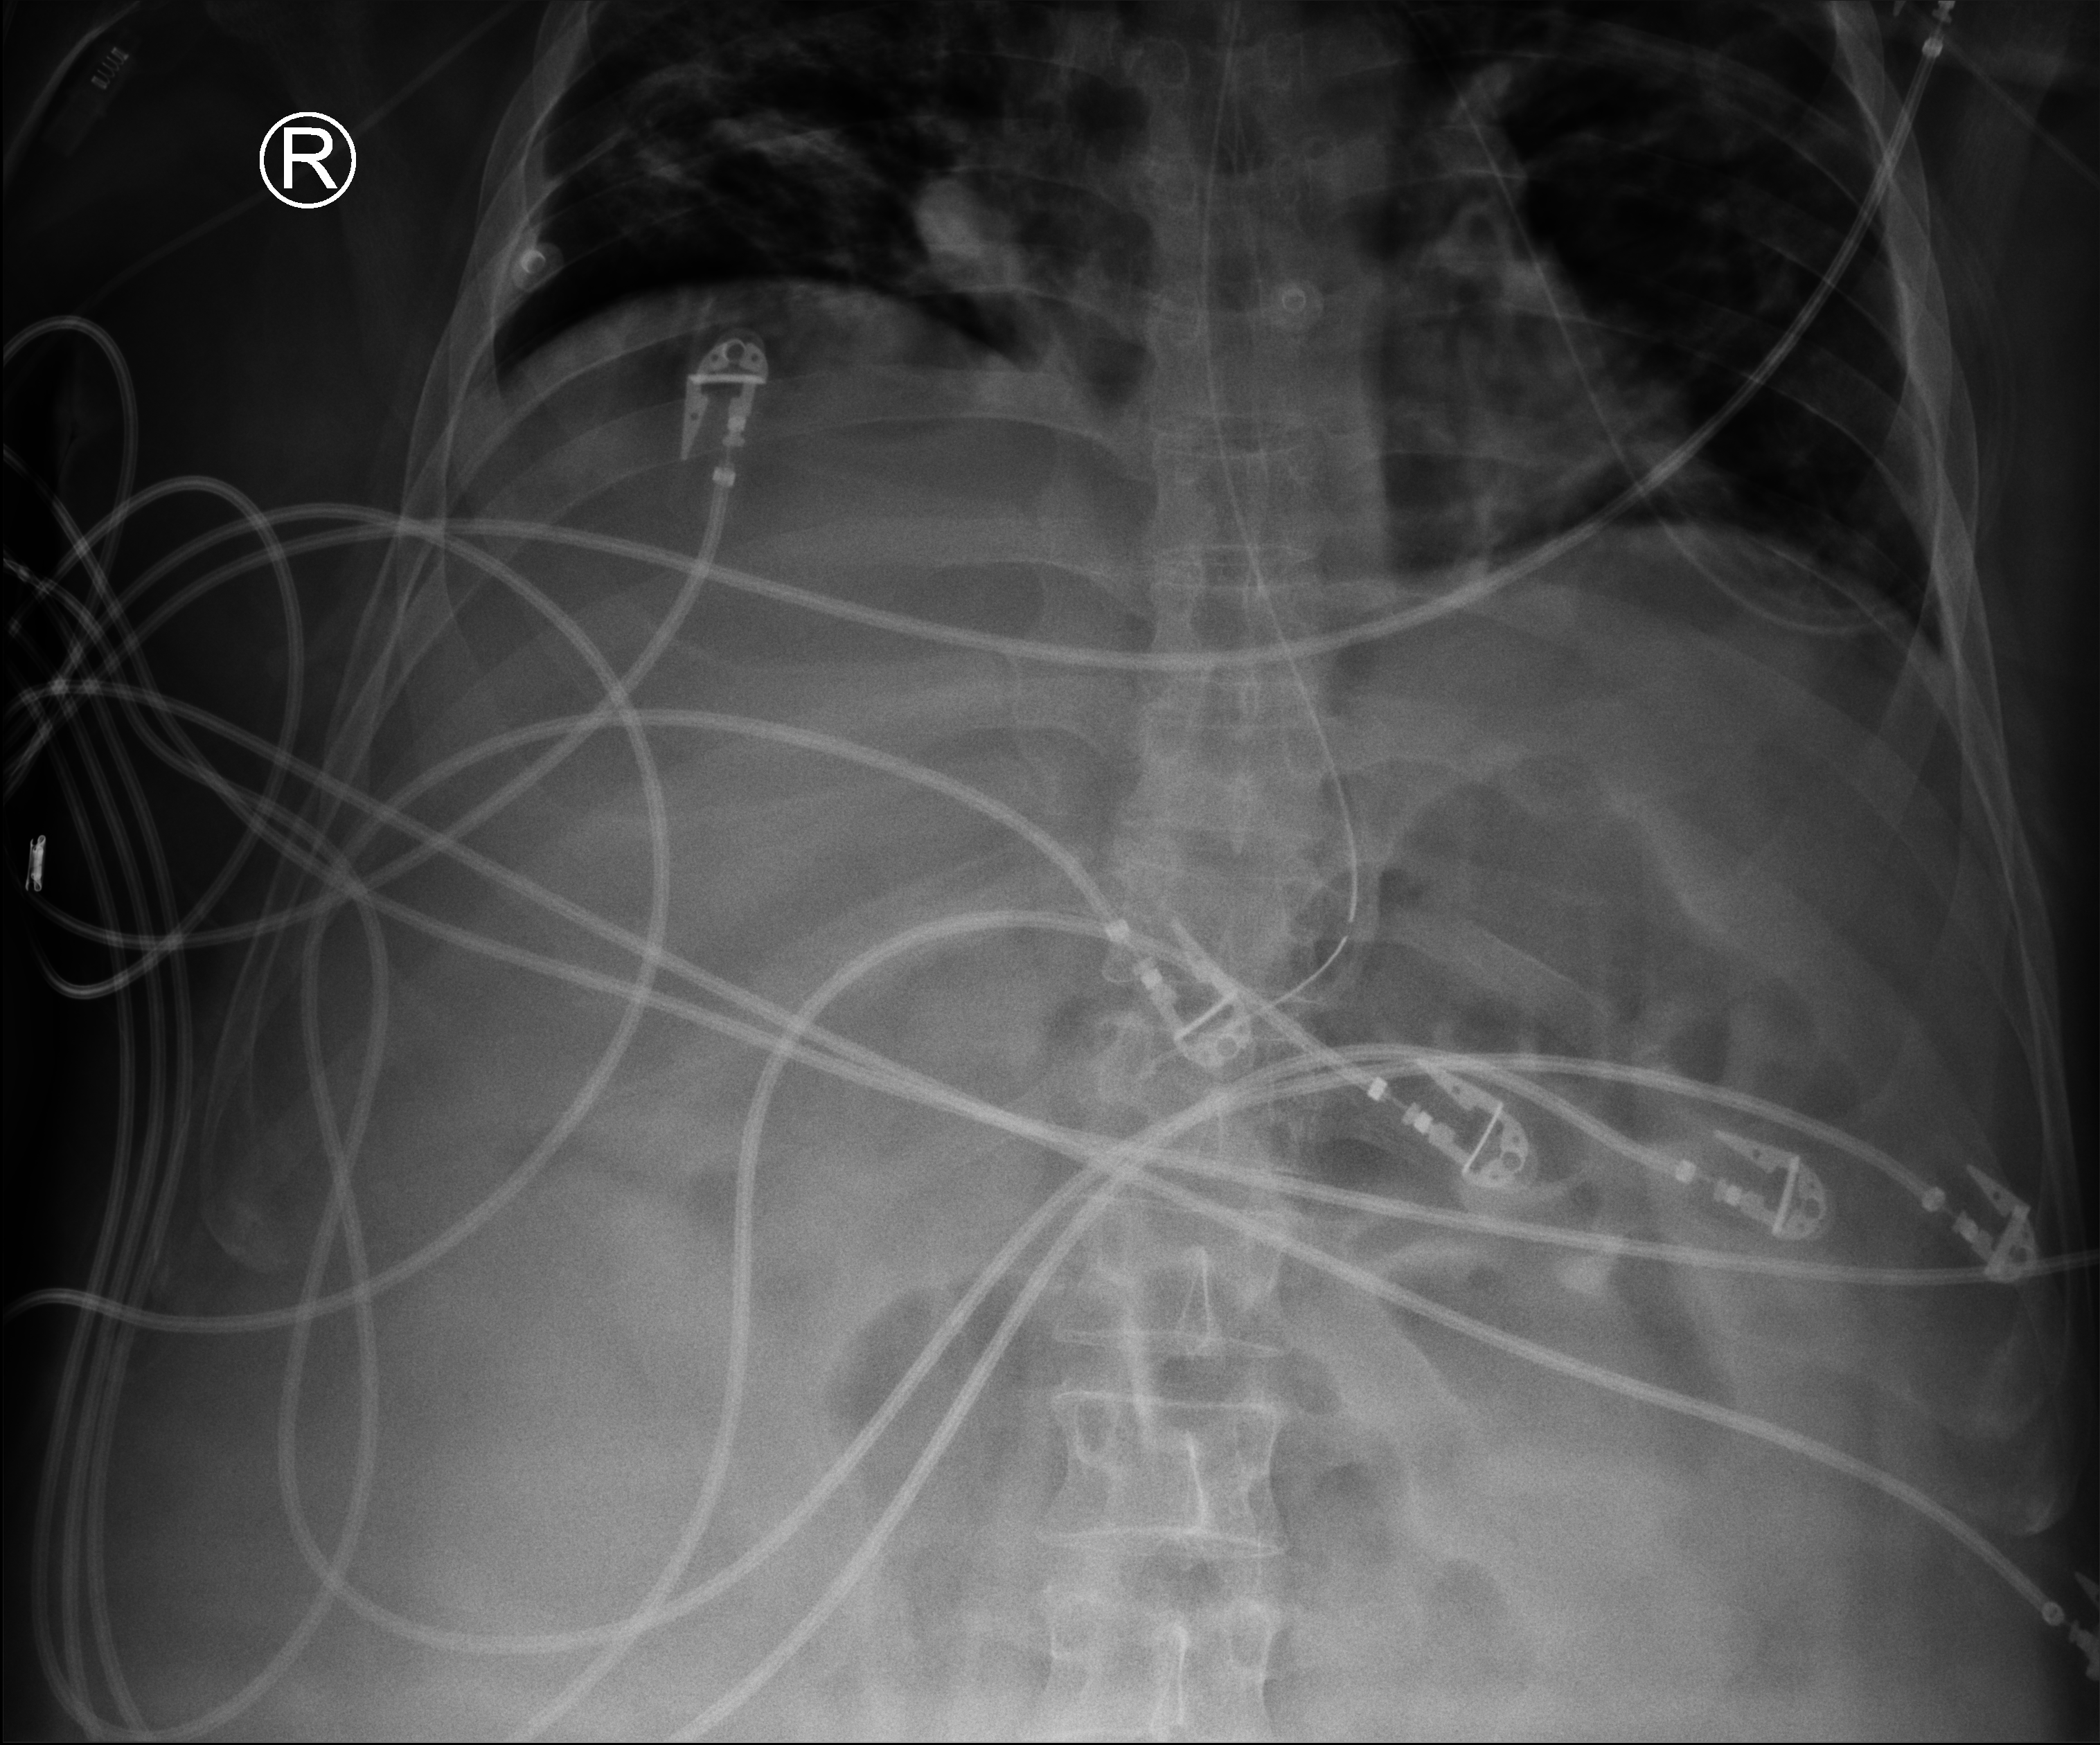
Bedside abdomen radiograph (computed radiography), anteroposterior (AP) projection. Patient hospitalised with COVID-19, aged 18–59 years.
Hospital-stay facts (about this admission, not read from this image; timing relative to this image not recorded): hypertension (admission record): yes.